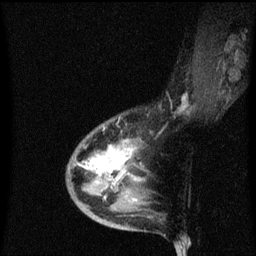
Breast MRI (dynamic contrast-enhanced), one sagittal slice; dynamic contrast-enhanced series, image 2 of 3 at this slice position (ordered by acquisition); 1.5 T; TE 4.2 ms, TR 8.4 ms; 2 mm slice thickness; 256 × 256 image matrix, field of view 200 × 200 mm. Female patient, age 38 years. From the clinical record (not read from this slice): setting: breast cancer imaged before/during neoadjuvant chemotherapy; receptor status: HR-positive, HER2-negative.
Annotated regions visible in this slice (semi-automatic segmentation, software-assisted and operator-edited):
- analysis volume of interest (the breast-tissue region the enhancement analysis was run in; not a lesion): bounding box [x1, y1, x2, y2] px = [68, 116, 149, 205]
- tumour enhancement mask (voxels above the 70 % enhancement threshold inside the analysis volume of interest): [82, 146, 133, 175]